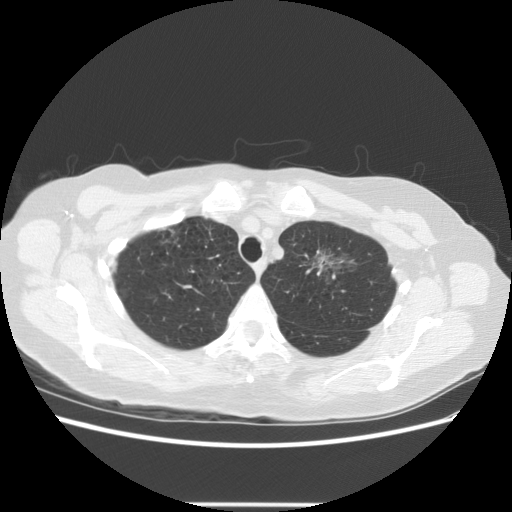
Axial slice from a low-dose chest CT screening exam, third annual screen, lung window (W 1500 / L -600 HU), 2.5 mm slice thickness, standard (soft-tissue) reconstruction kernel (STANDARD), slice 103 of 126 in the series, 512 × 512 image matrix, field of view 360 × 360 mm. Female, age 65 years at enrolment.
• Lesion marked by an expert reader, bounding box (x1, y1, x2, y2) in pixels: (291, 229, 367, 294).
• Screening reader's record for this exam (one nodule recorded; not confirmed to be the boxed lesion): non-calcified nodule or mass ≥4 mm, left upper lobe, 17 × 14 mm, poorly defined margins, ground glass attenuation, pre-existing on the prior screen: yes; interval growth: yes.
• Official screen result: positive, other.
• Later outcome: lung cancer diagnosed 96 days after this screen — adenocarcinoma, NOS, left upper lobe, moderately differentiated (G2), stage IA (AJCC 6th edition), 30 mm at pathology.